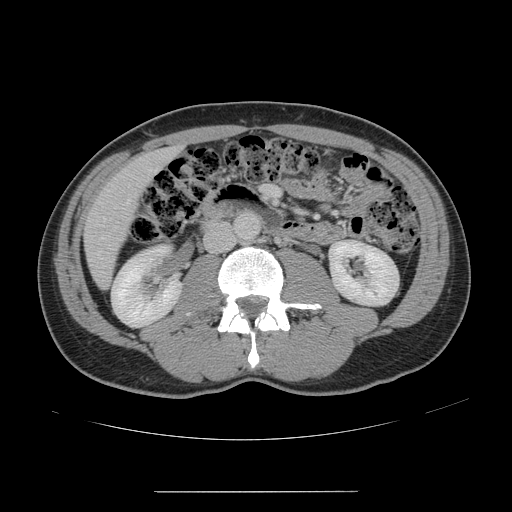
Contrast-enhanced abdominal CT, one axial slice. Position 45 of 178 along the scan axis. 120 kVp. Intravenous contrast given. Soft-tissue window (W 400 / L 40 HU). 2.5 mm slice thickness. 512 × 512 image matrix. Male patient, age 53 years. Case-level facts recorded for this patient, not image findings: diagnosis: colorectal cancer liver metastases, imaged before liver resection; multiple liver metastases: yes; largest metastasis: 2.4 cm; disease in both lobes: no.
Annotated regions visible in this slice (expert manual segmentation):
- hepatic veins: bounding box [x1, y1, x2, y2] px = [98, 169, 157, 260]
- liver: [85, 148, 177, 287]